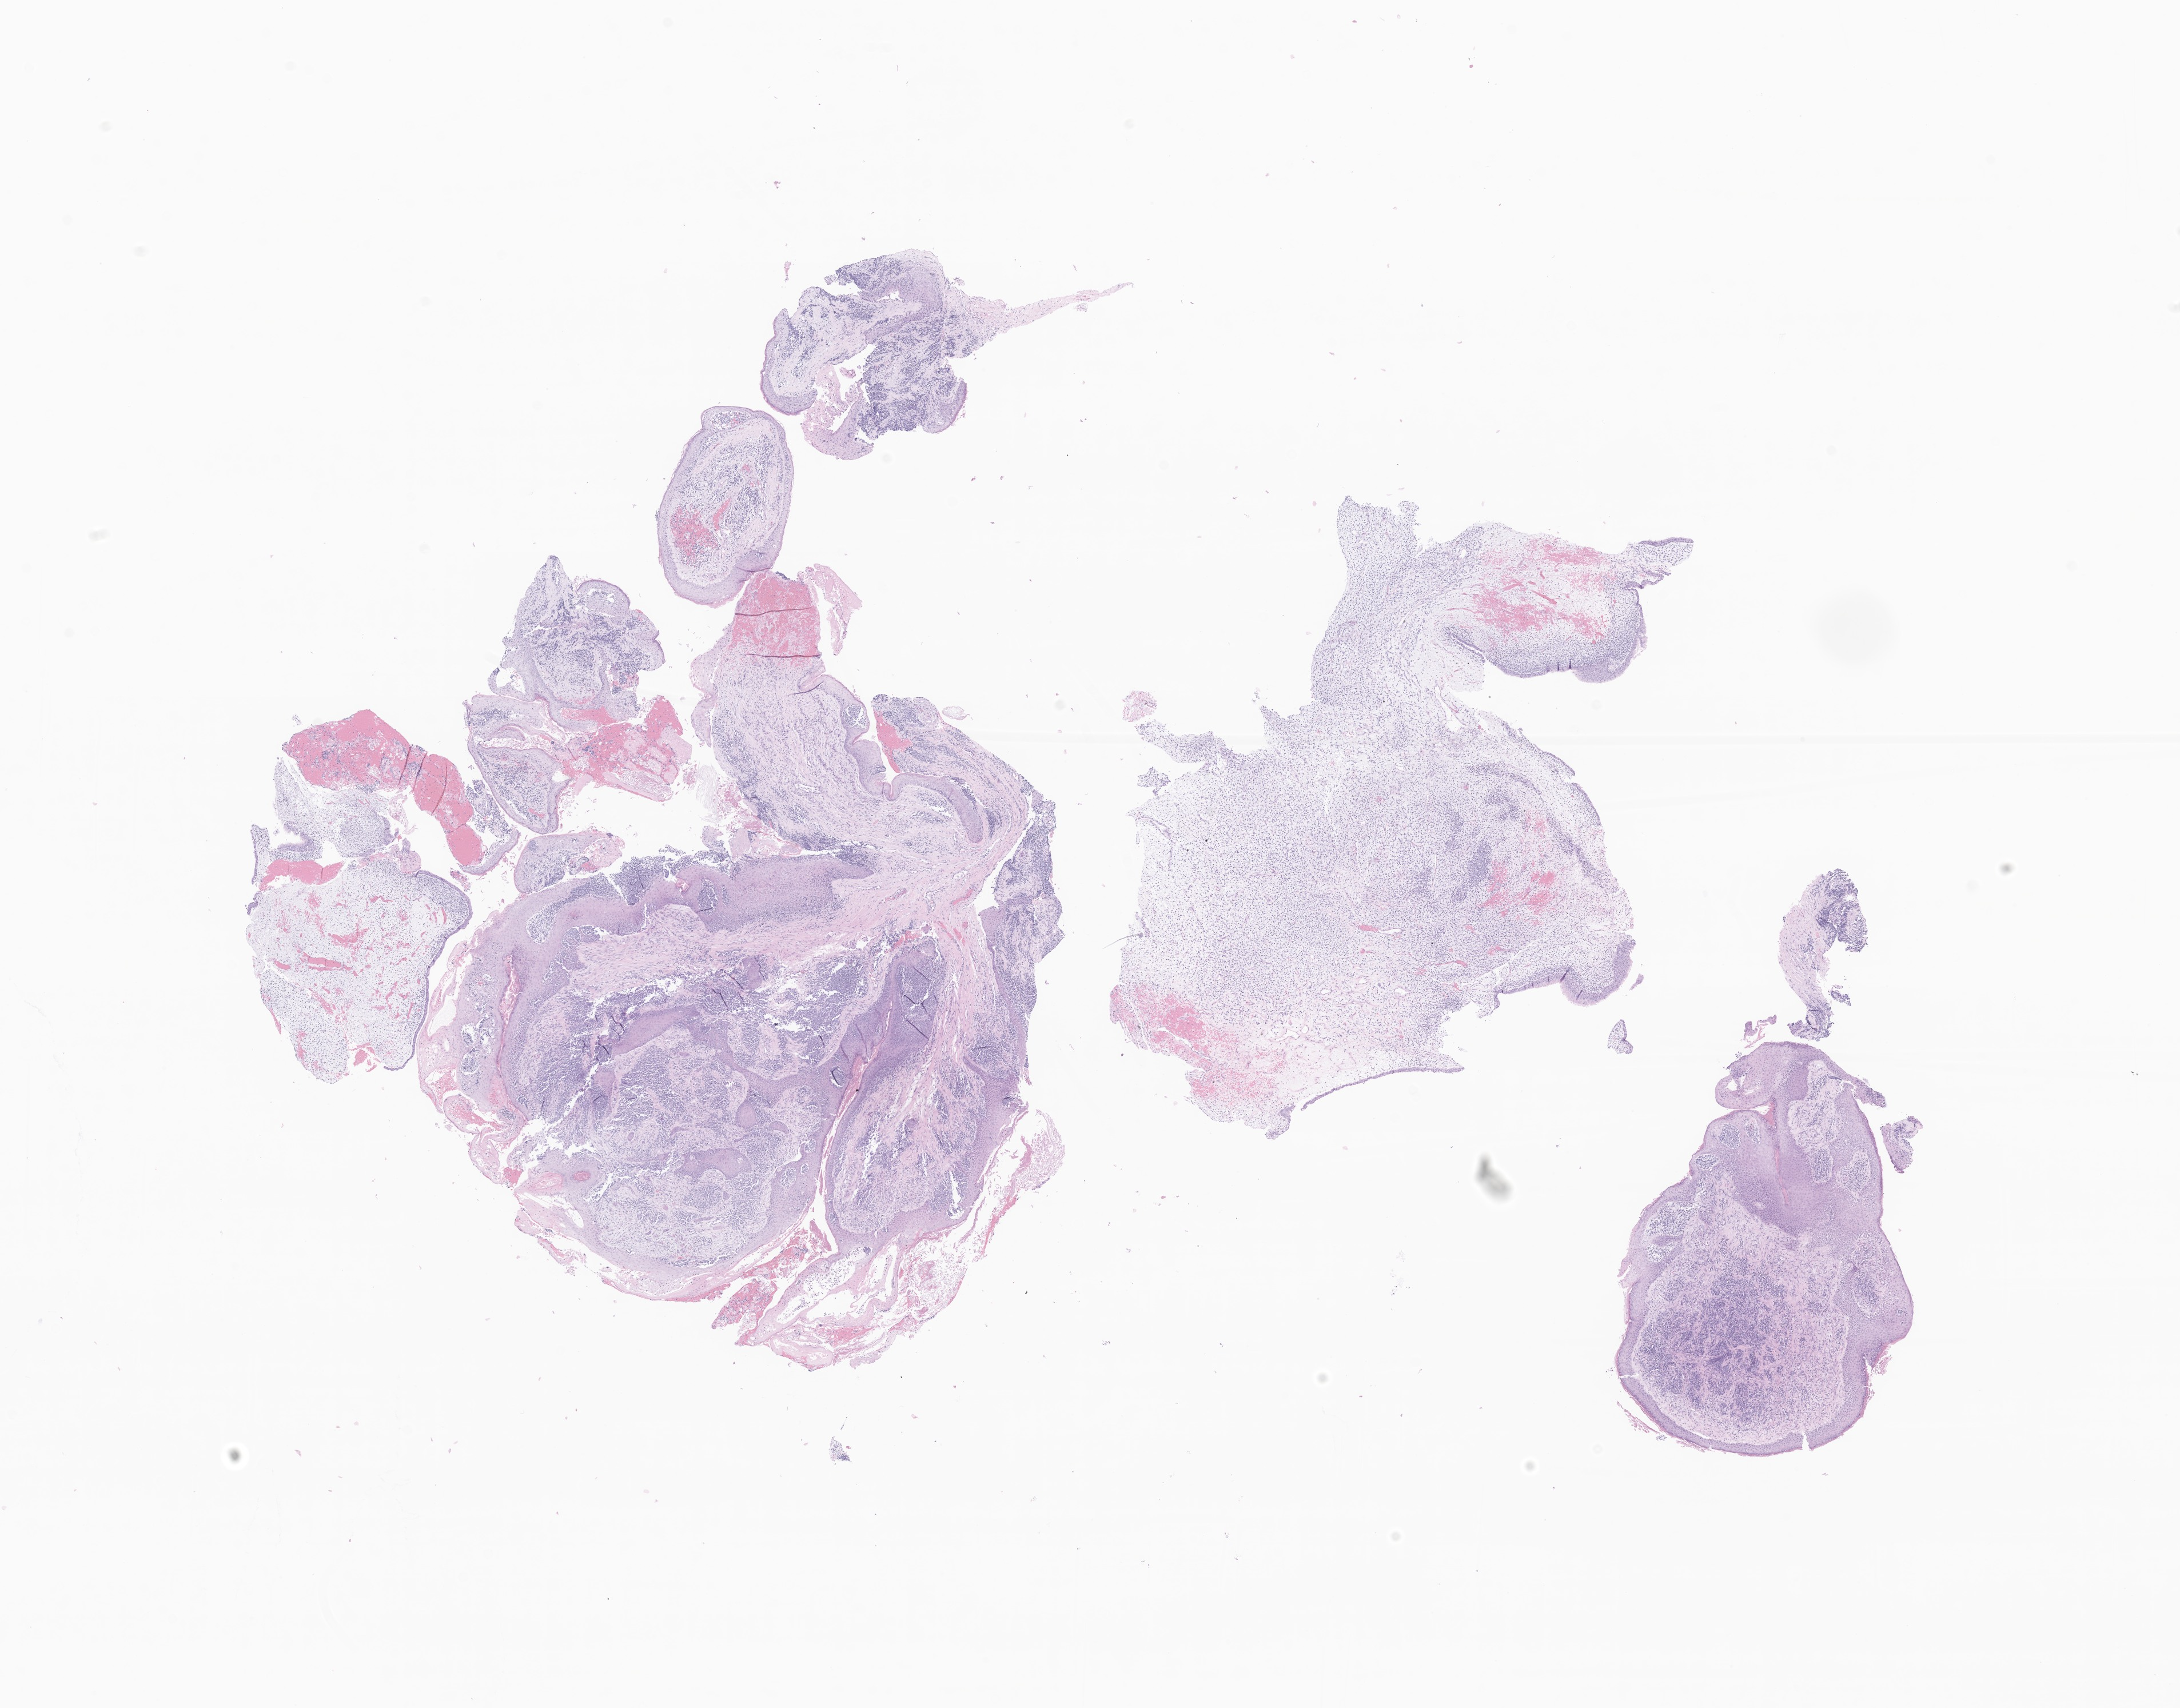
Whole-slide image, hematoxylin and eosin (H&E) stain of tumor tissue from the external ear, a low-resolution overview of the entire scanned area, about 16.1 x 12.6 mm, formalin-fixed paraffin-embedded section. Patient: male, age 539 days.
Diagnosis (ICD-O-3 morphology term): Embryonal rhabdomyosarcoma, NOS.